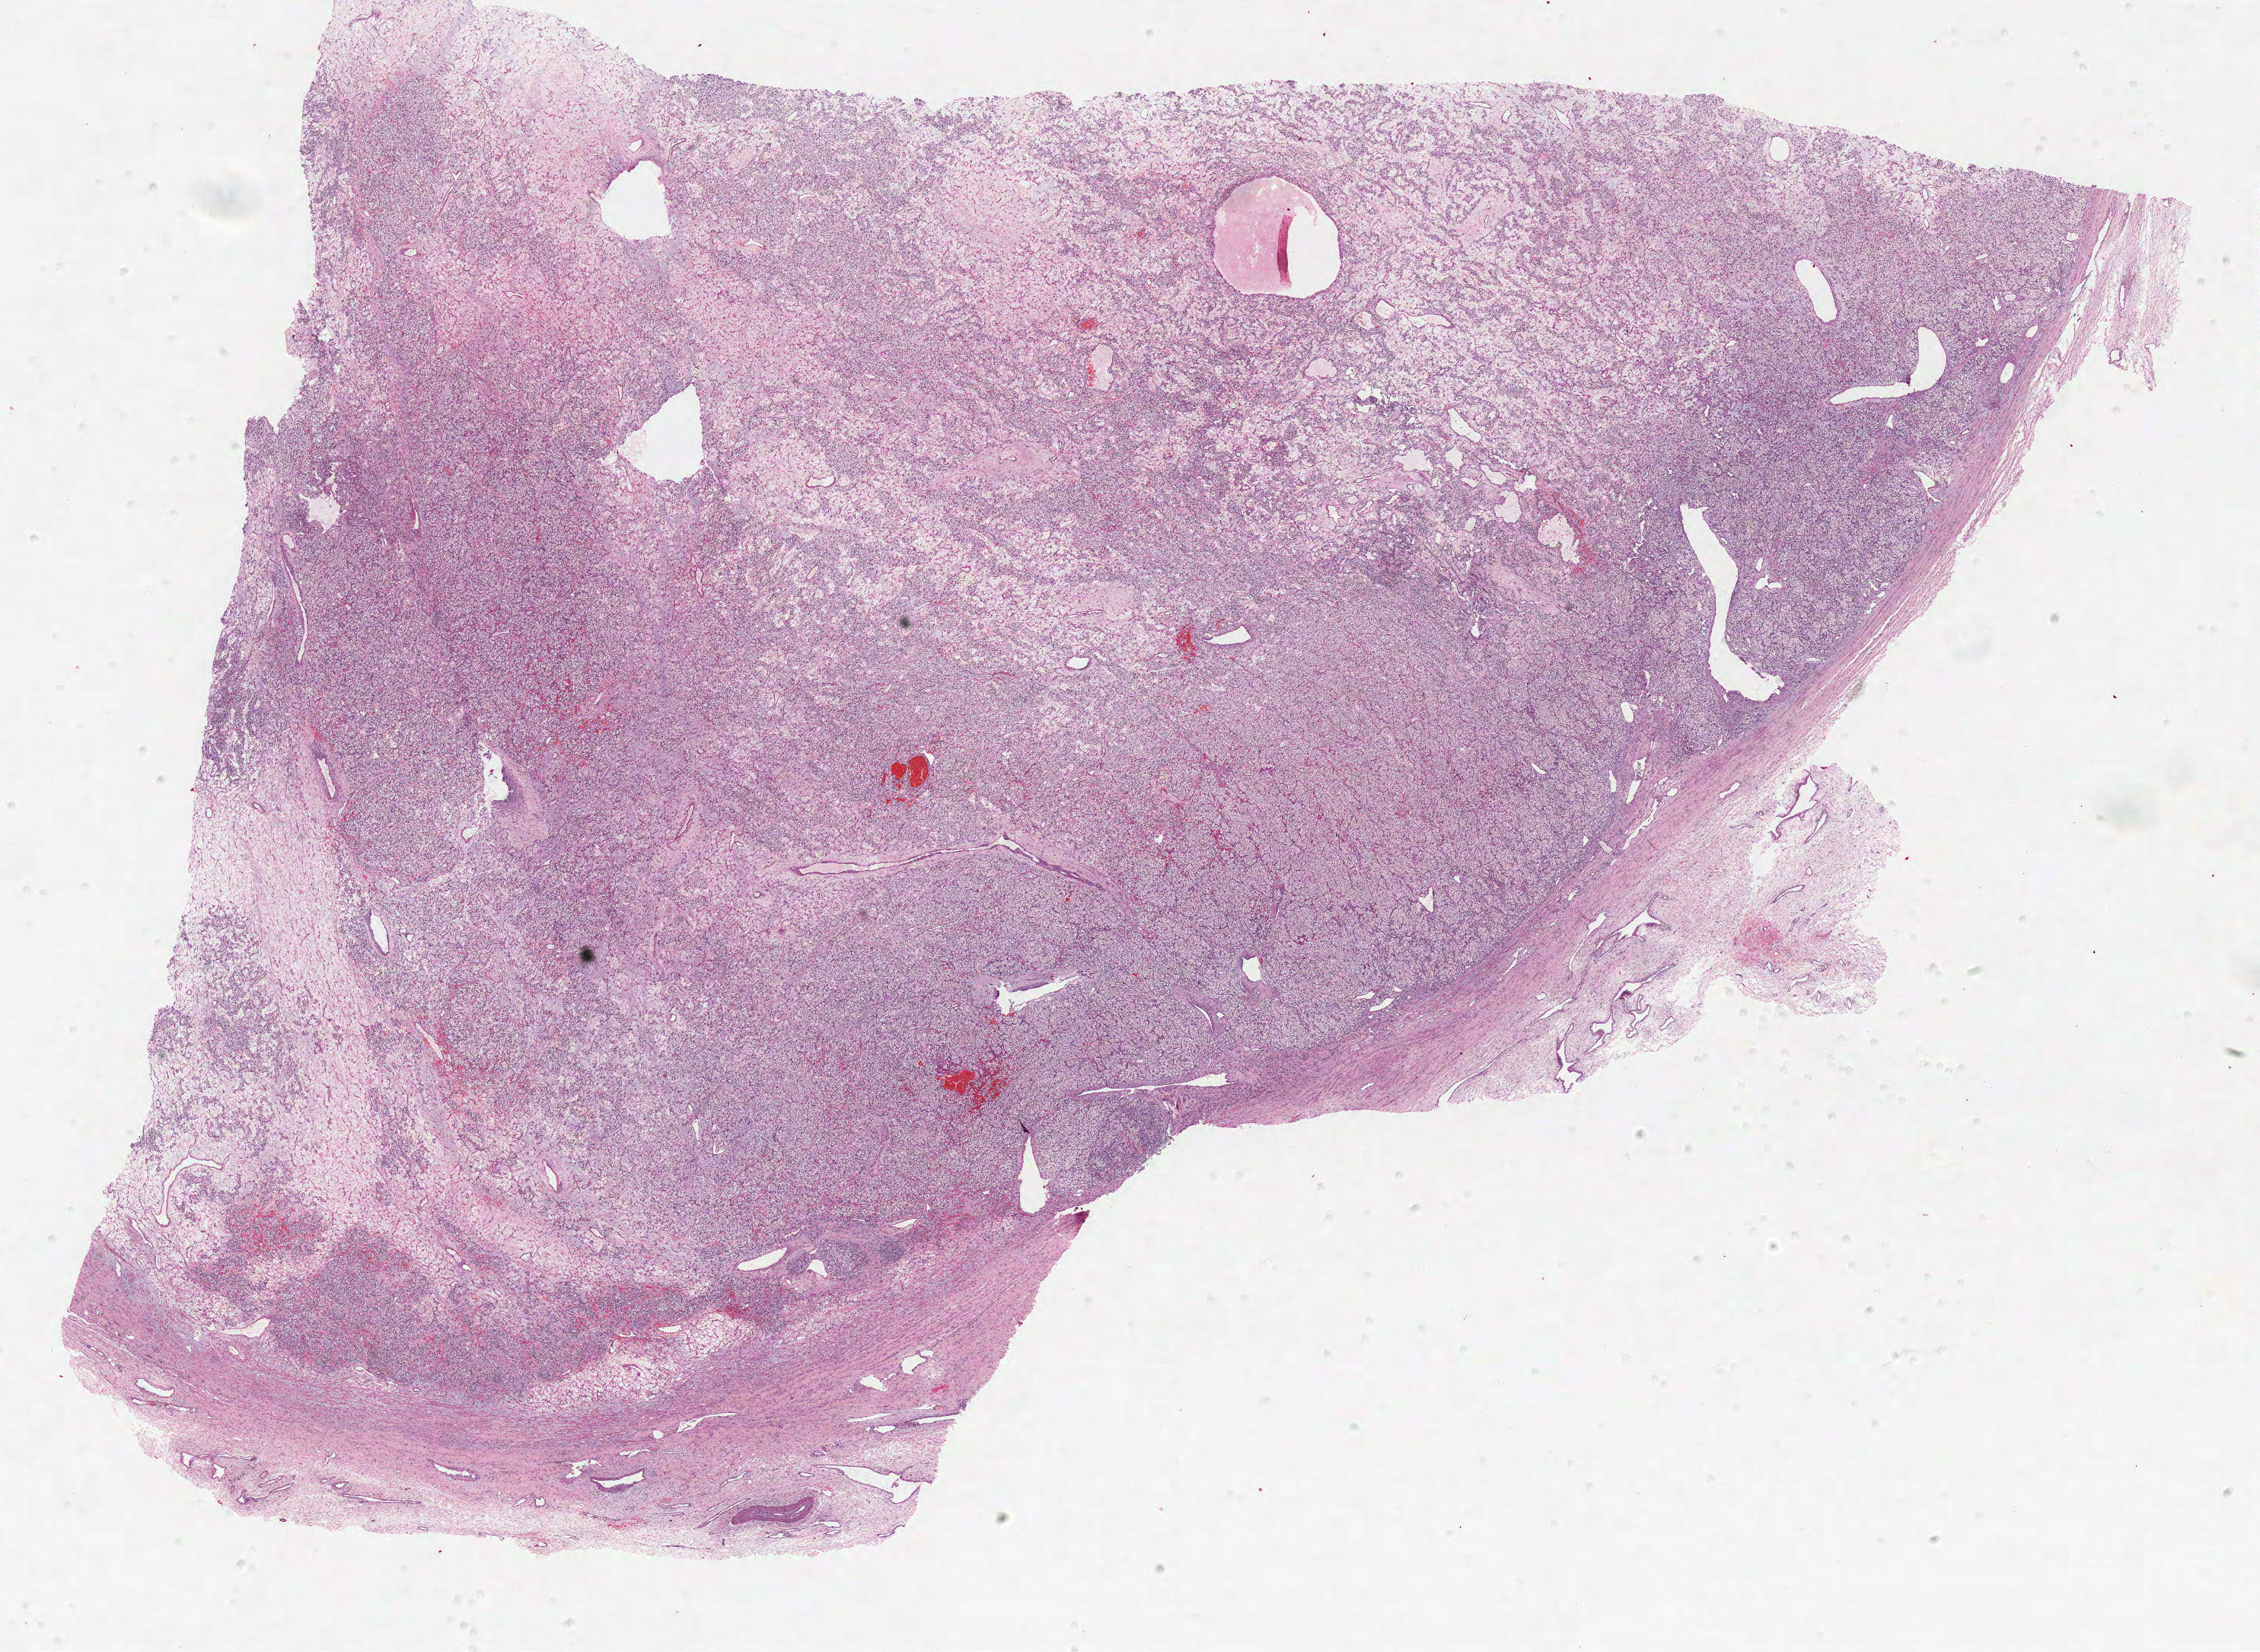
Digitized Hematoxylin and eosin (H&E) stained tissue section (whole slide), shown as a low-resolution overview of the whole scanned area (about 23.7 x 17.3 mm, acquisition: 40x scan). Formalin-fixed paraffin-embedded (FFPE) diagnostic section. Primary tumour sample from the kidney. Female patient; age at initial diagnosis 41 years. Histologic grade: G2 (moderately differentiated).
- histologic diagnosis: Clear cell adenocarcinoma, NOS
- laterality: left
- AJCC pathologic stage: I